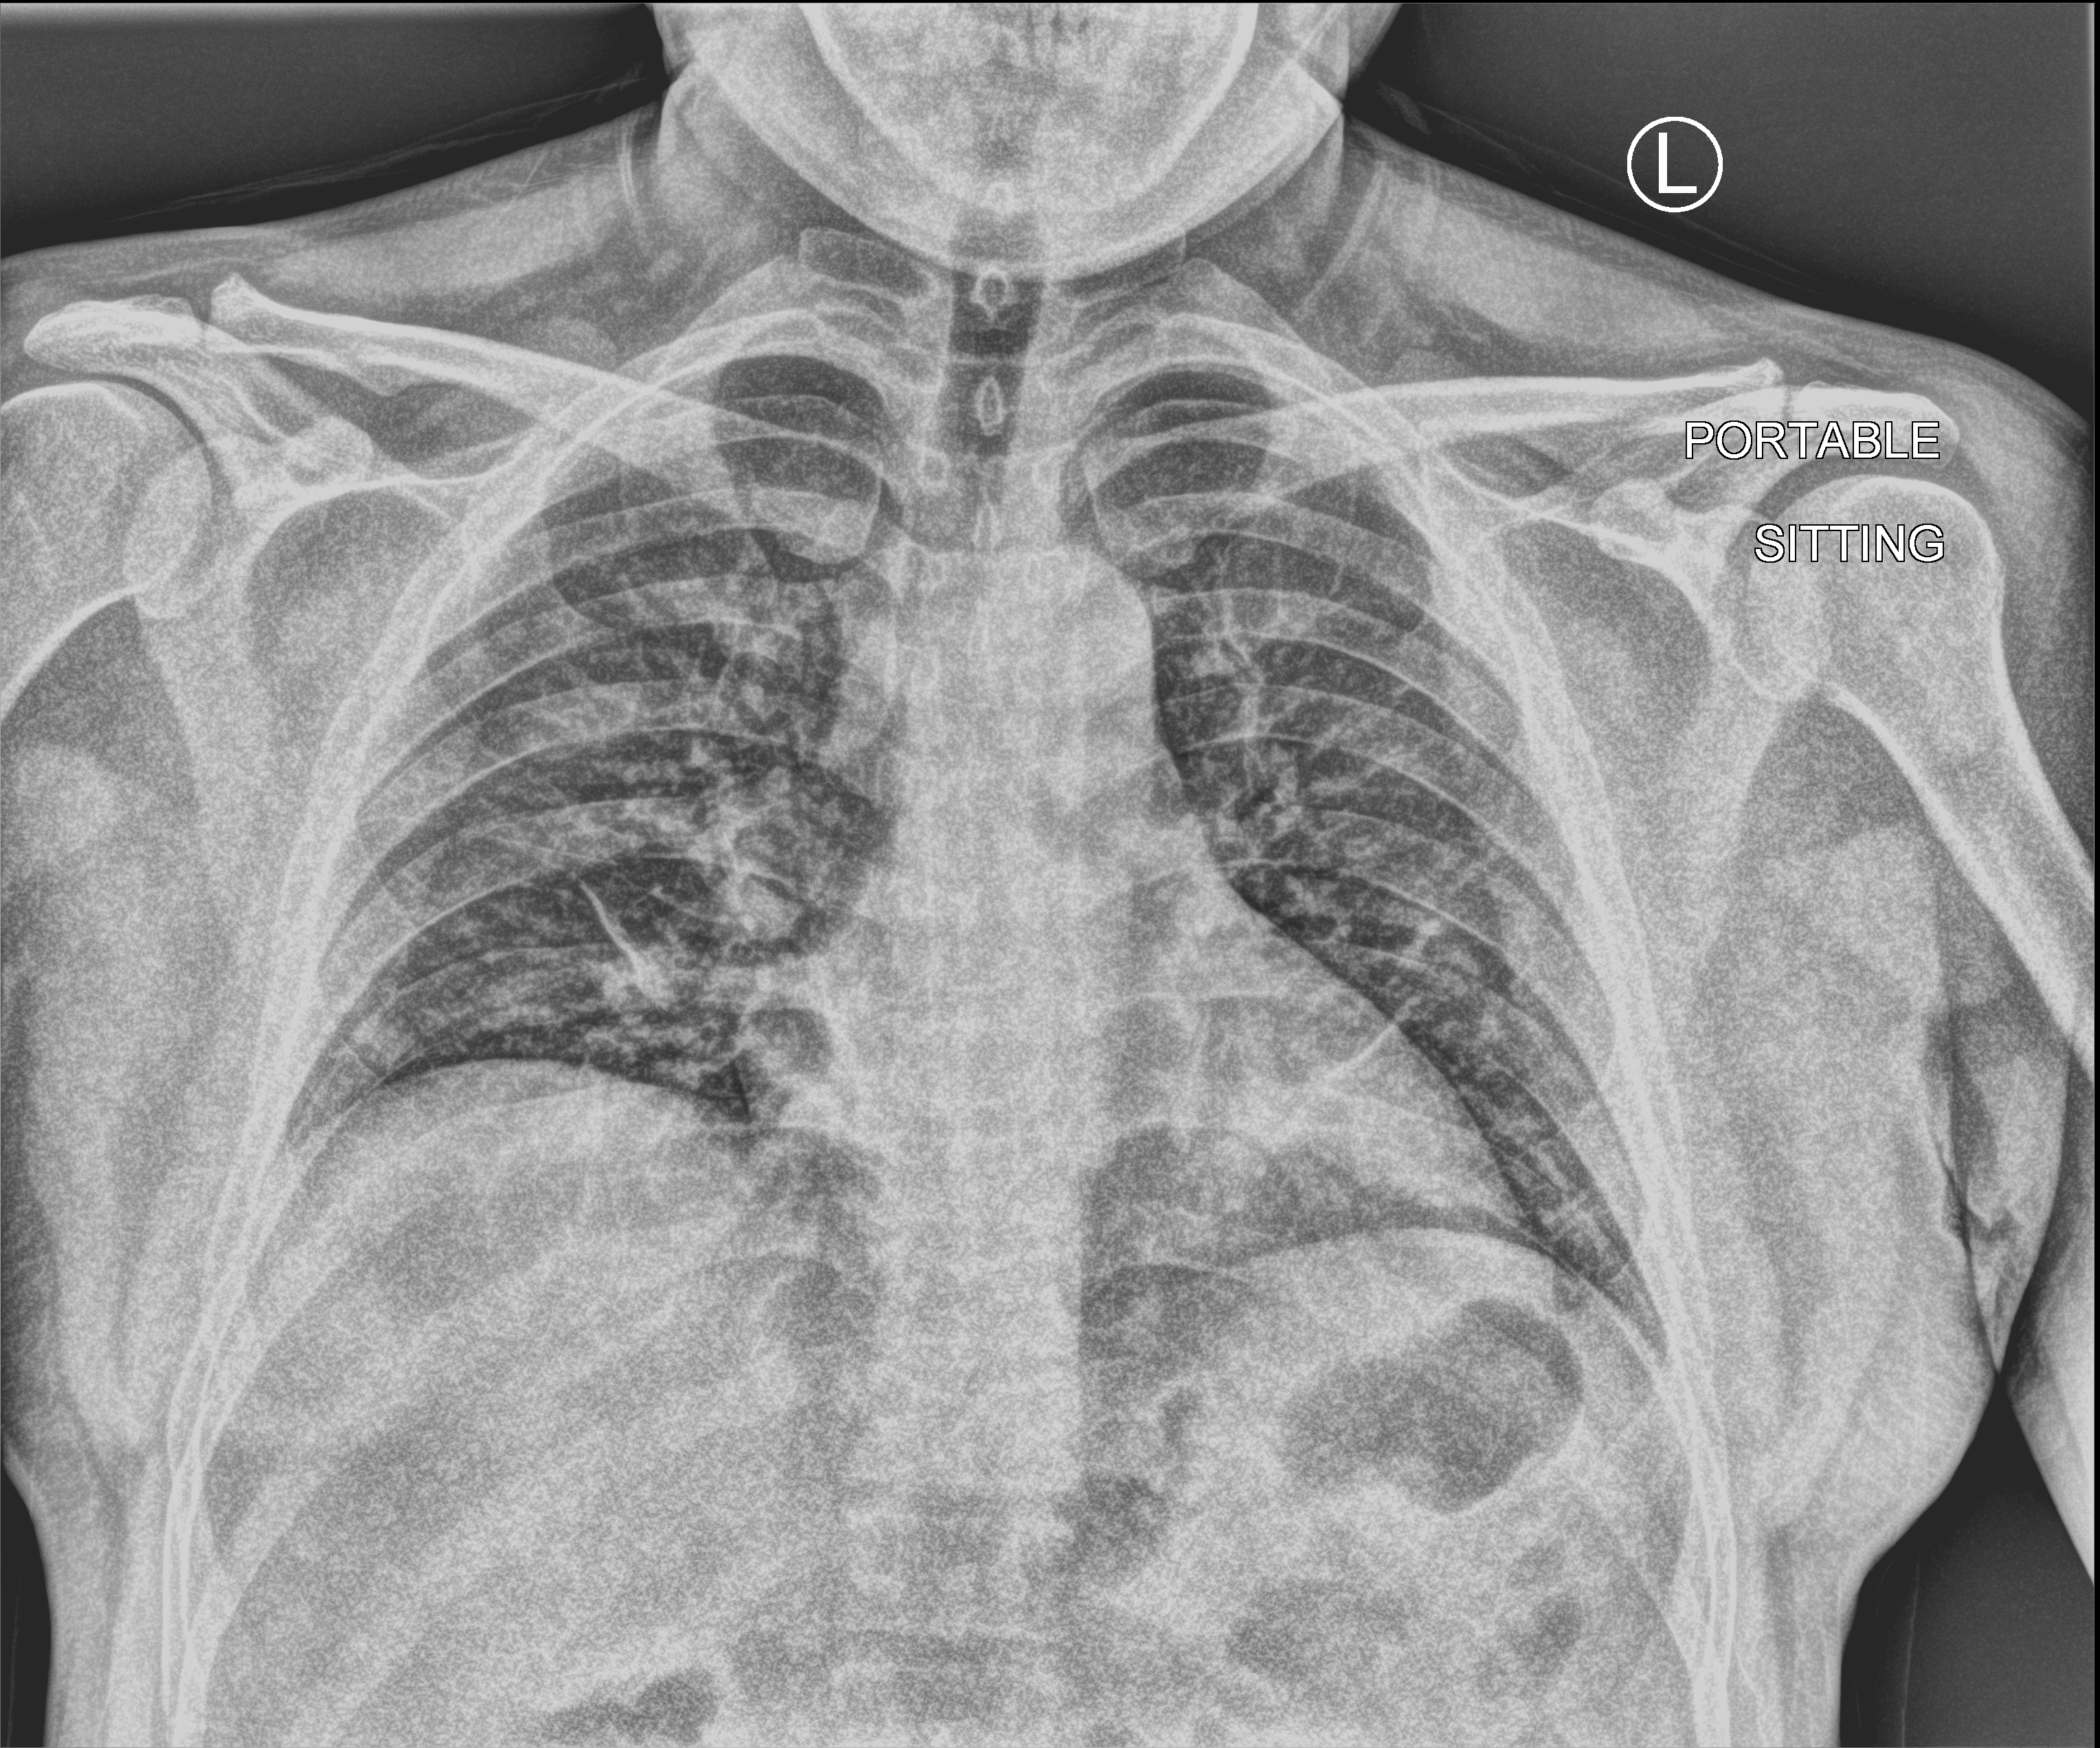
Bedside chest radiograph (computed radiography); anteroposterior (AP) projection. Male patient hospitalised with COVID-19, age 18–59 years.
Hospital-stay facts (about this admission, not read from this image; timing relative to this image not recorded): mechanically ventilated during this hospital stay: no.